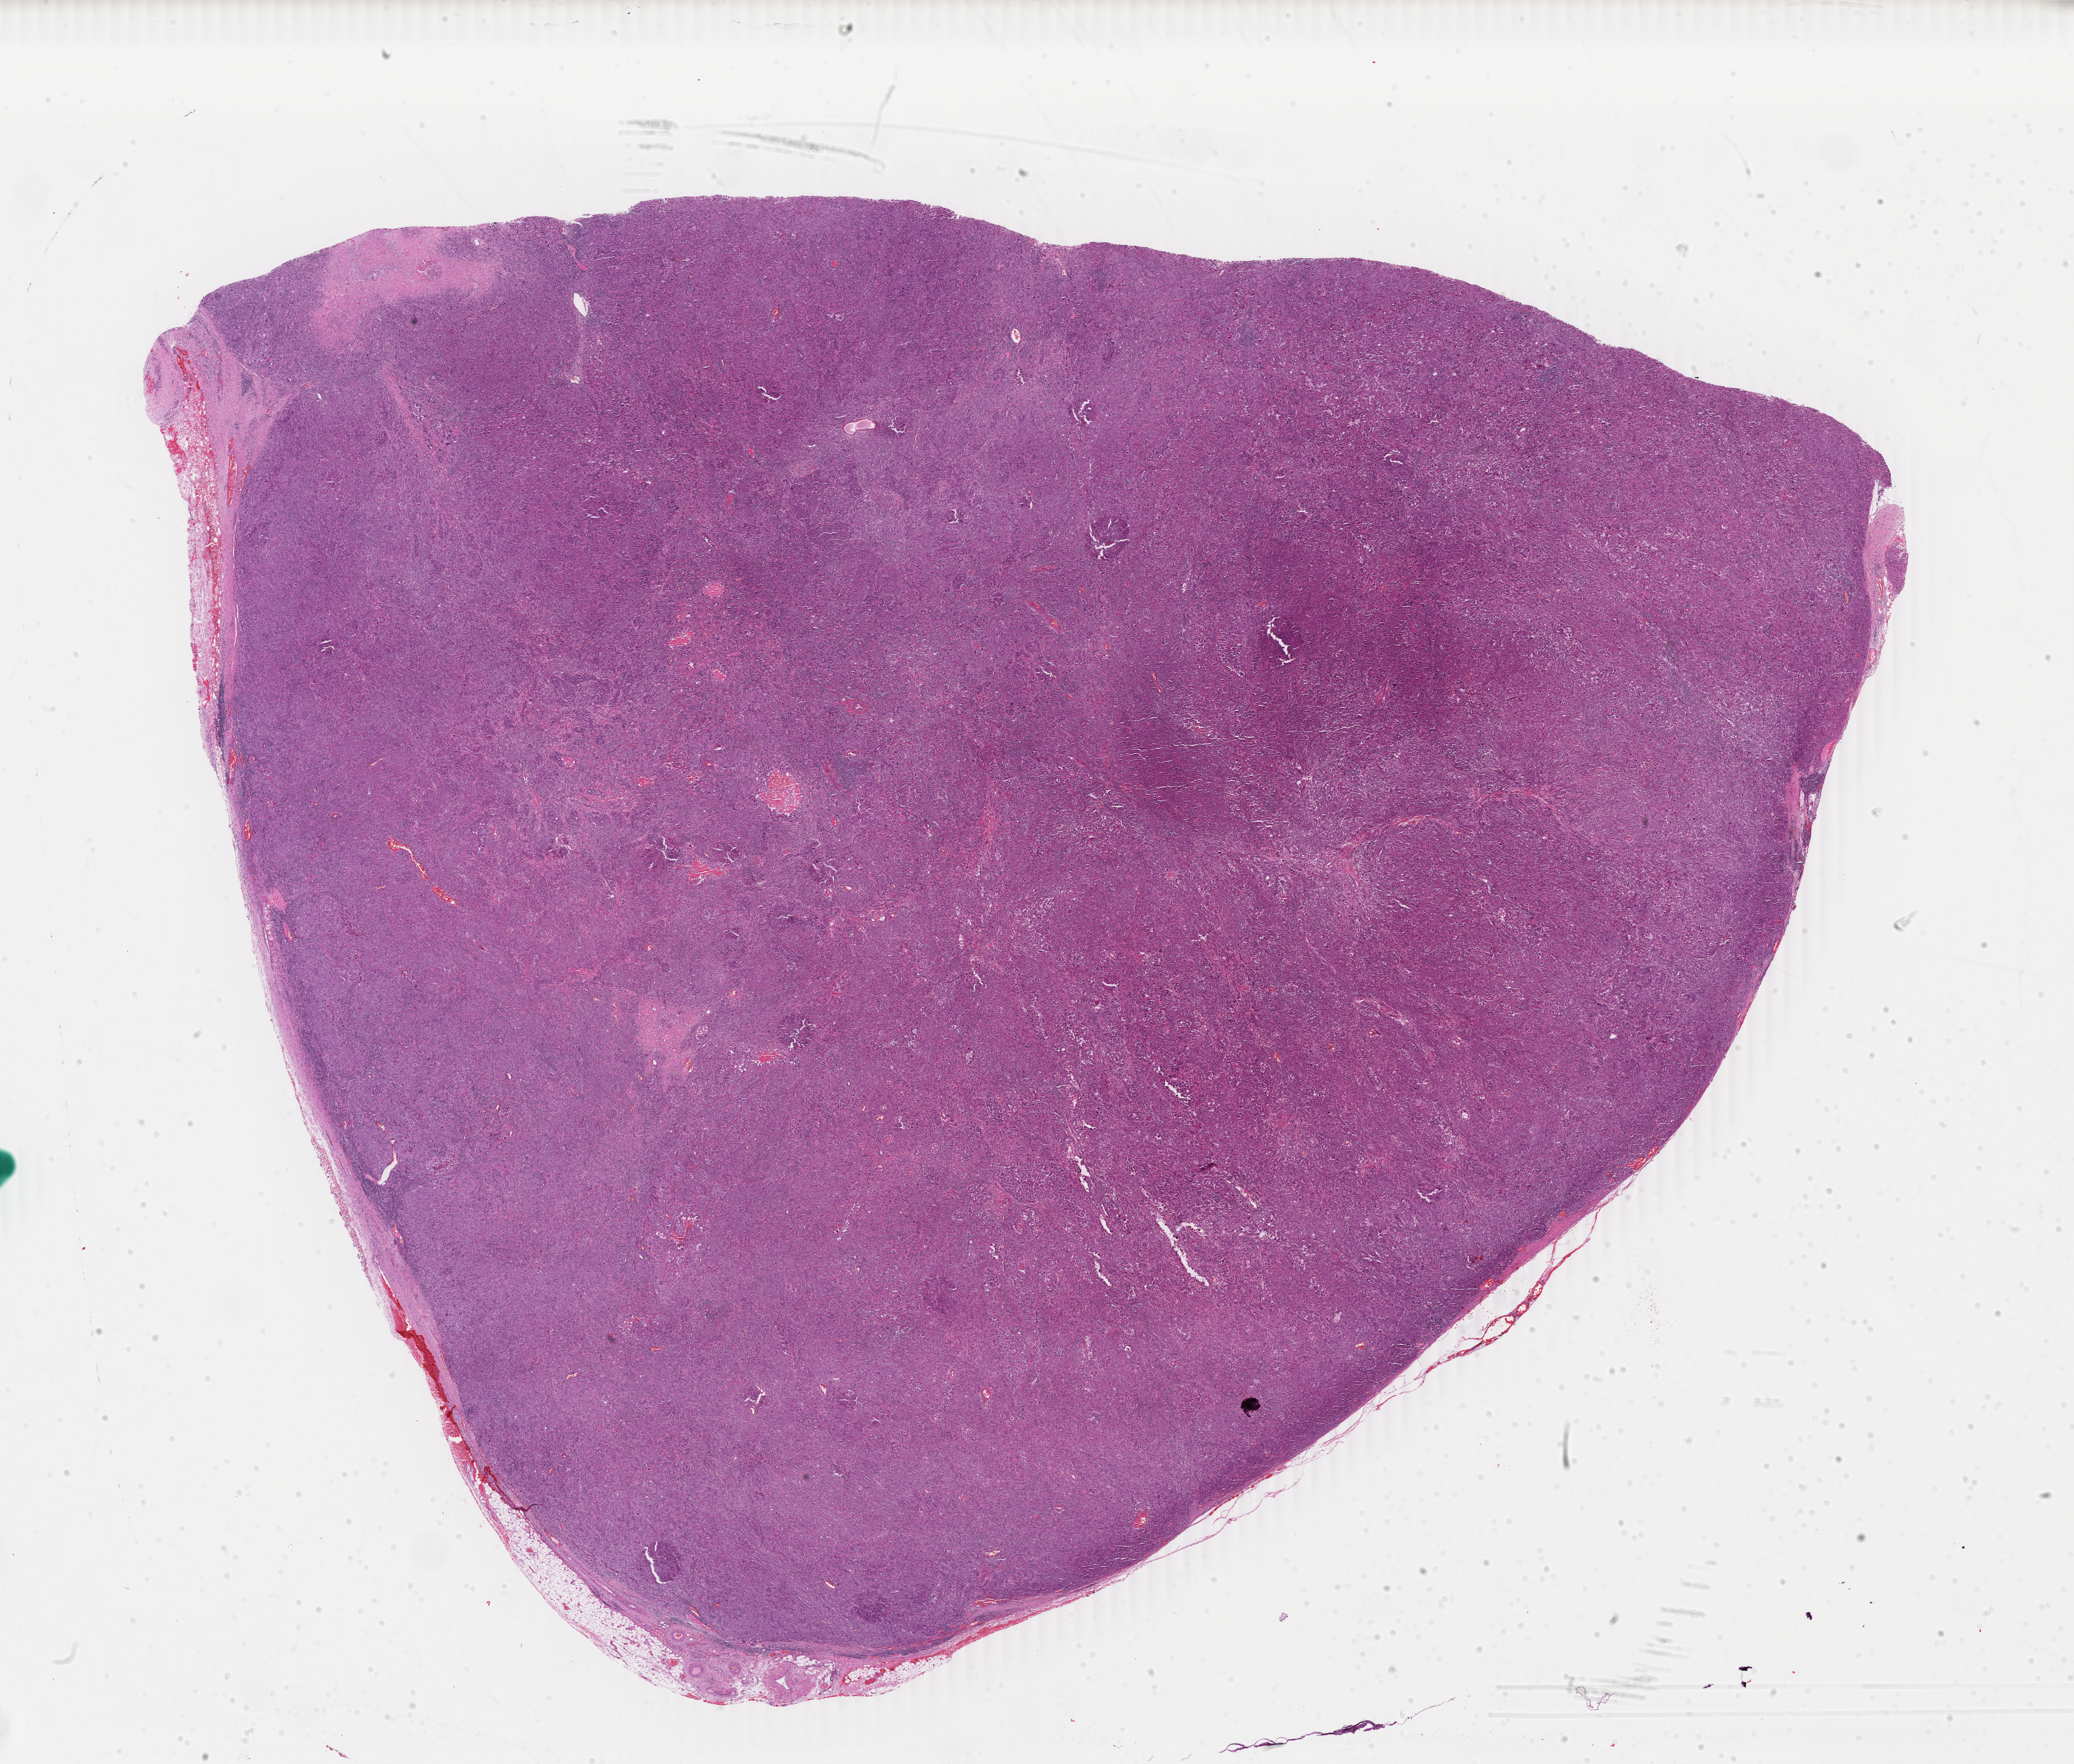
Digitized H&E-stained tissue section (whole slide), low-resolution overview of the scanned area, about 27.1 x 23.1 mm (acquisition: 40x scan), formalin-fixed paraffin-embedded (FFPE) diagnostic section, sample: primary tumour, skin. Male, age 82 years at initial diagnosis.
Diagnosis: Malignant melanoma, NOS.